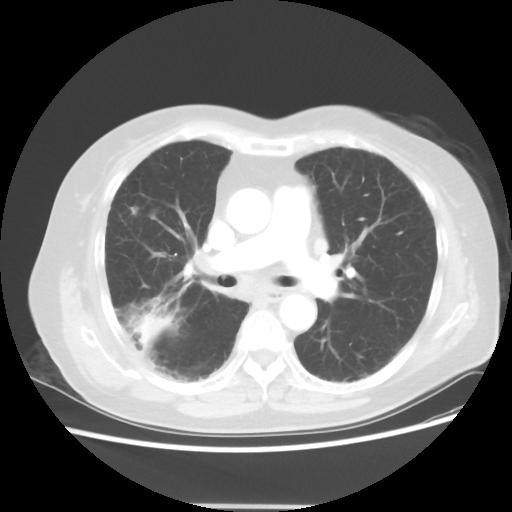
Chest CT, one axial slice. Slice 28 of 50 in the series (ordered by position). Reconstruction kernel STANDARD. 120 kVp. Lung window (W 1500 / L -600 HU). 5 mm slice thickness. 512 × 512 image matrix. Patient: female, 72 years. From the clinical record (not read from this slice): clinical TNM (as recorded): T2 N1 M0.
Annotated regions visible in this slice (bounding box drawn by a radiologist):
- lung tumour (recorded histology: adenocarcinoma): bounding box (x1, y1, x2, y2) in pixels: (126, 311, 171, 345)